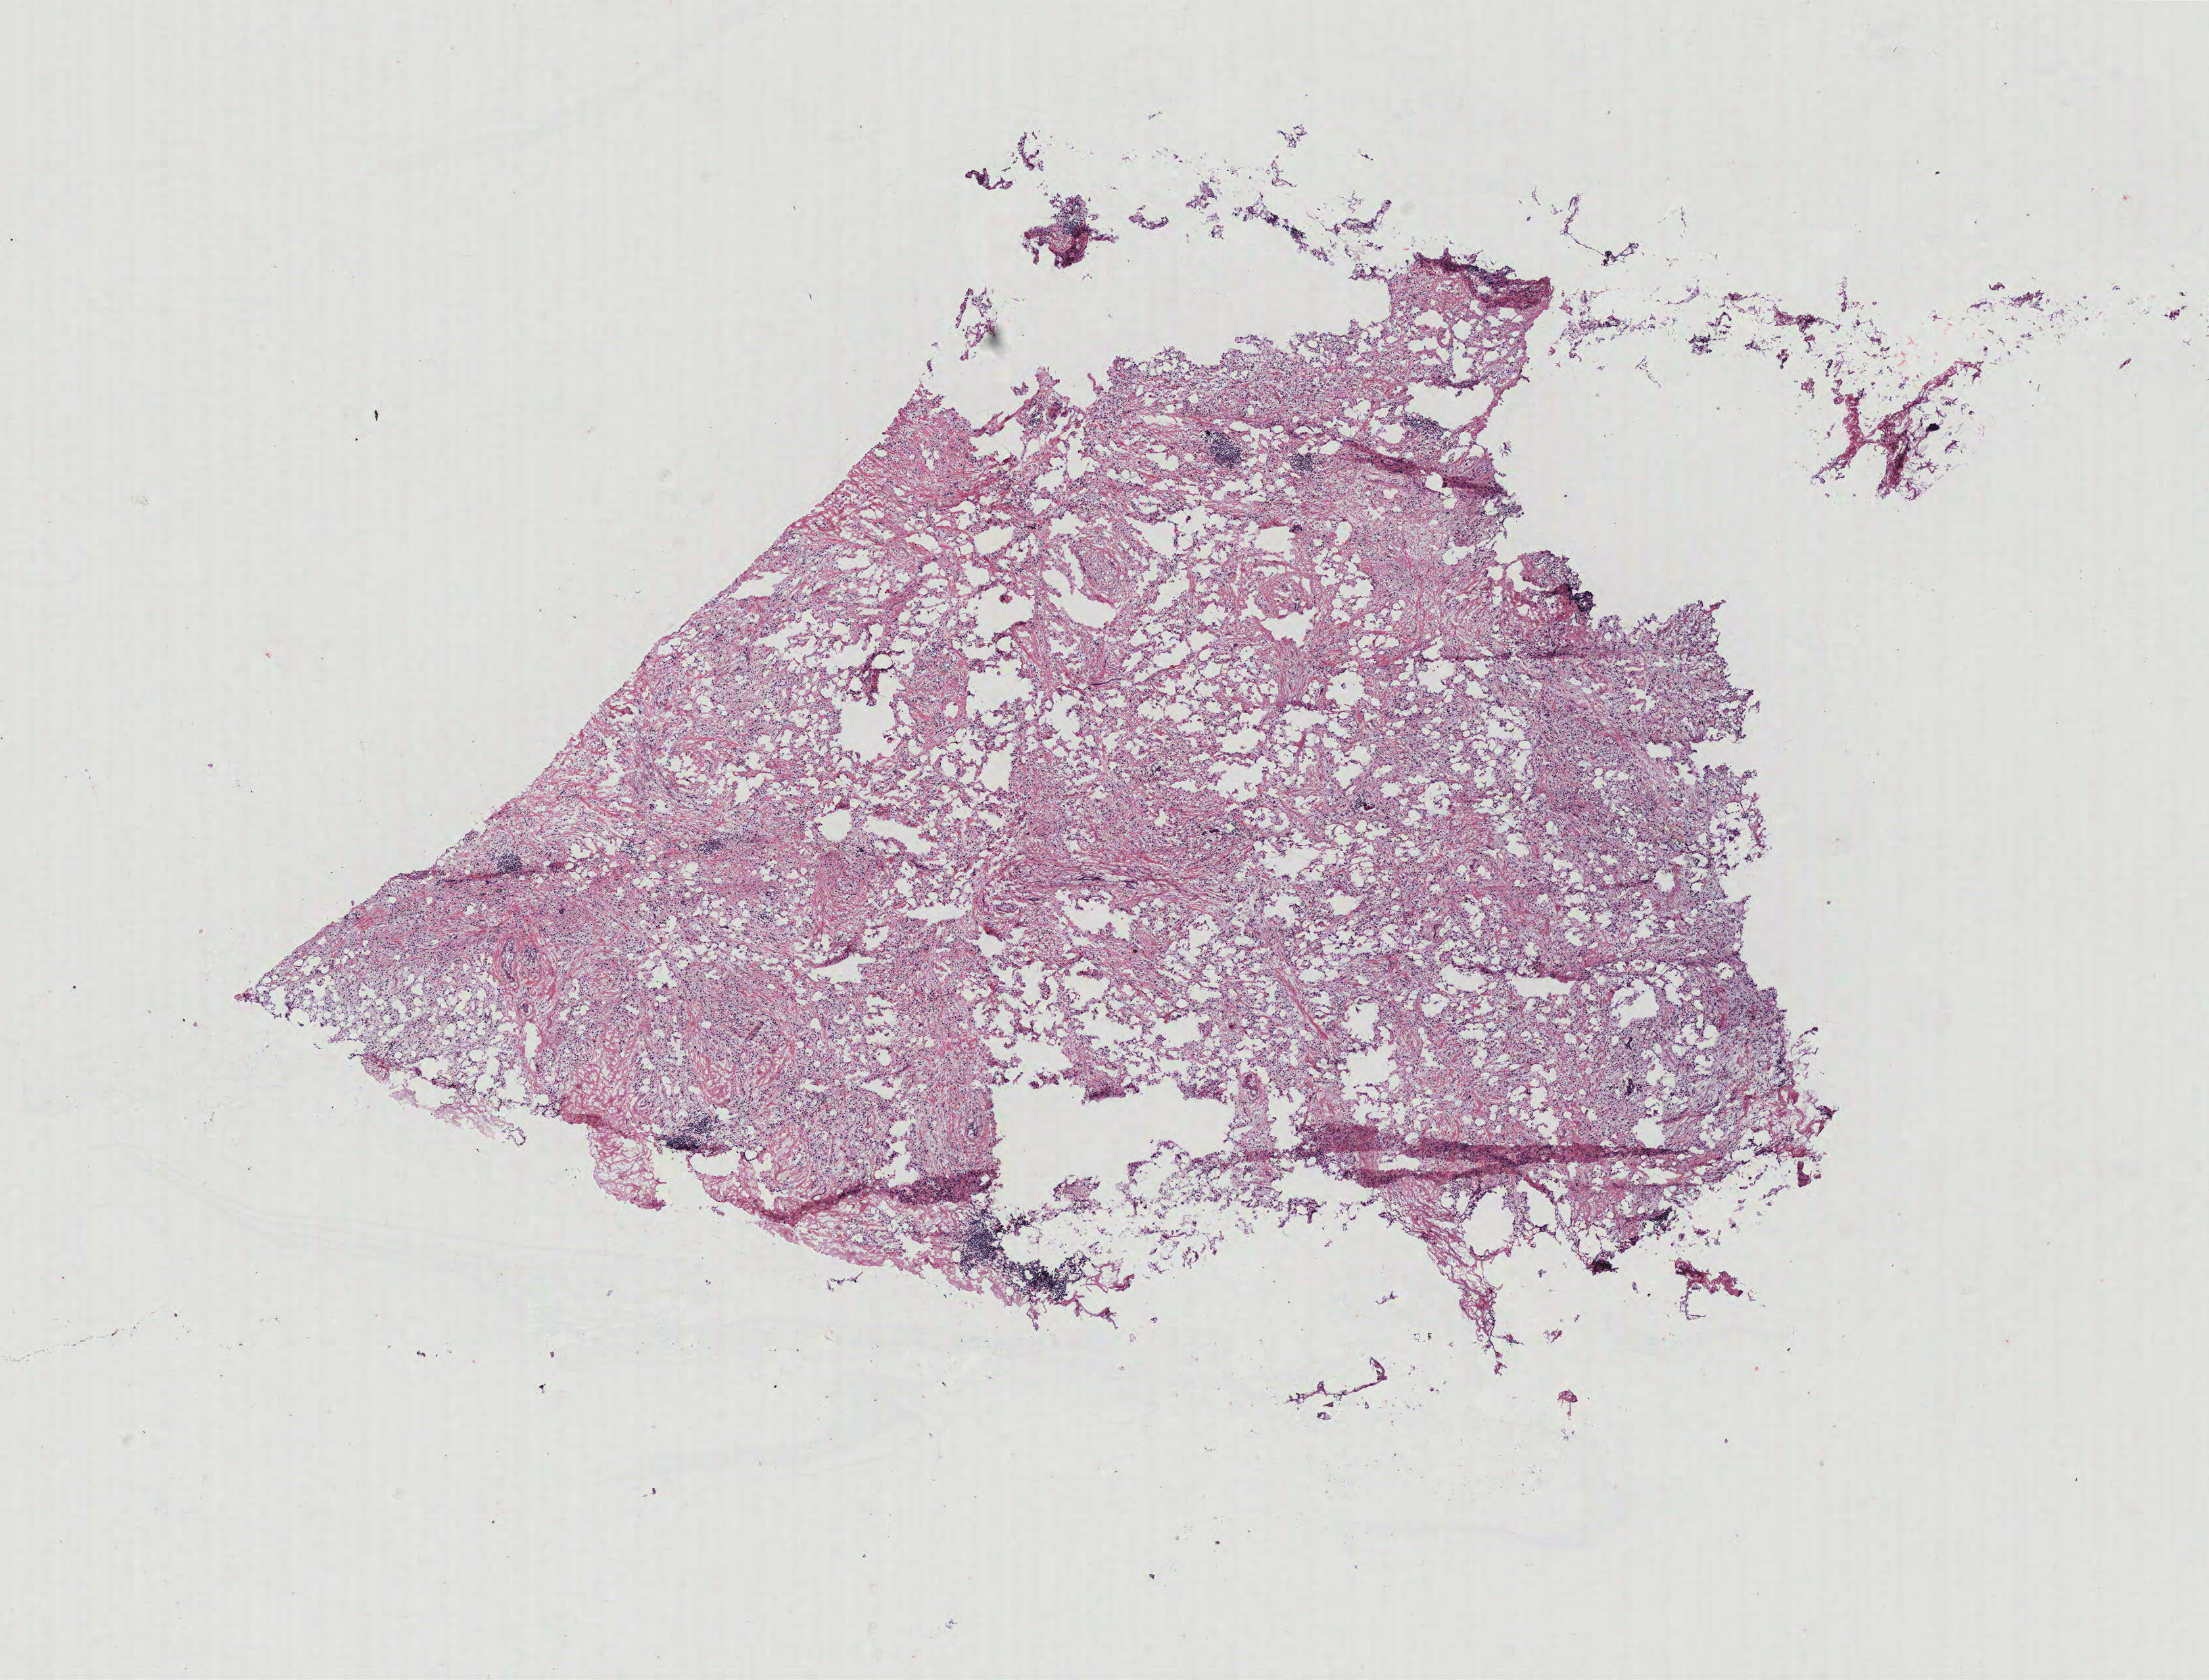
Whole-slide histology image, H&E — a low-resolution overview of the entire scanned area, about 13.4 x 10.2 mm (from a 40x scan). Breast, tissue type not recorded. Patient sex: female.
* patient diagnosis: Infiltrating duct carcinoma, NOS